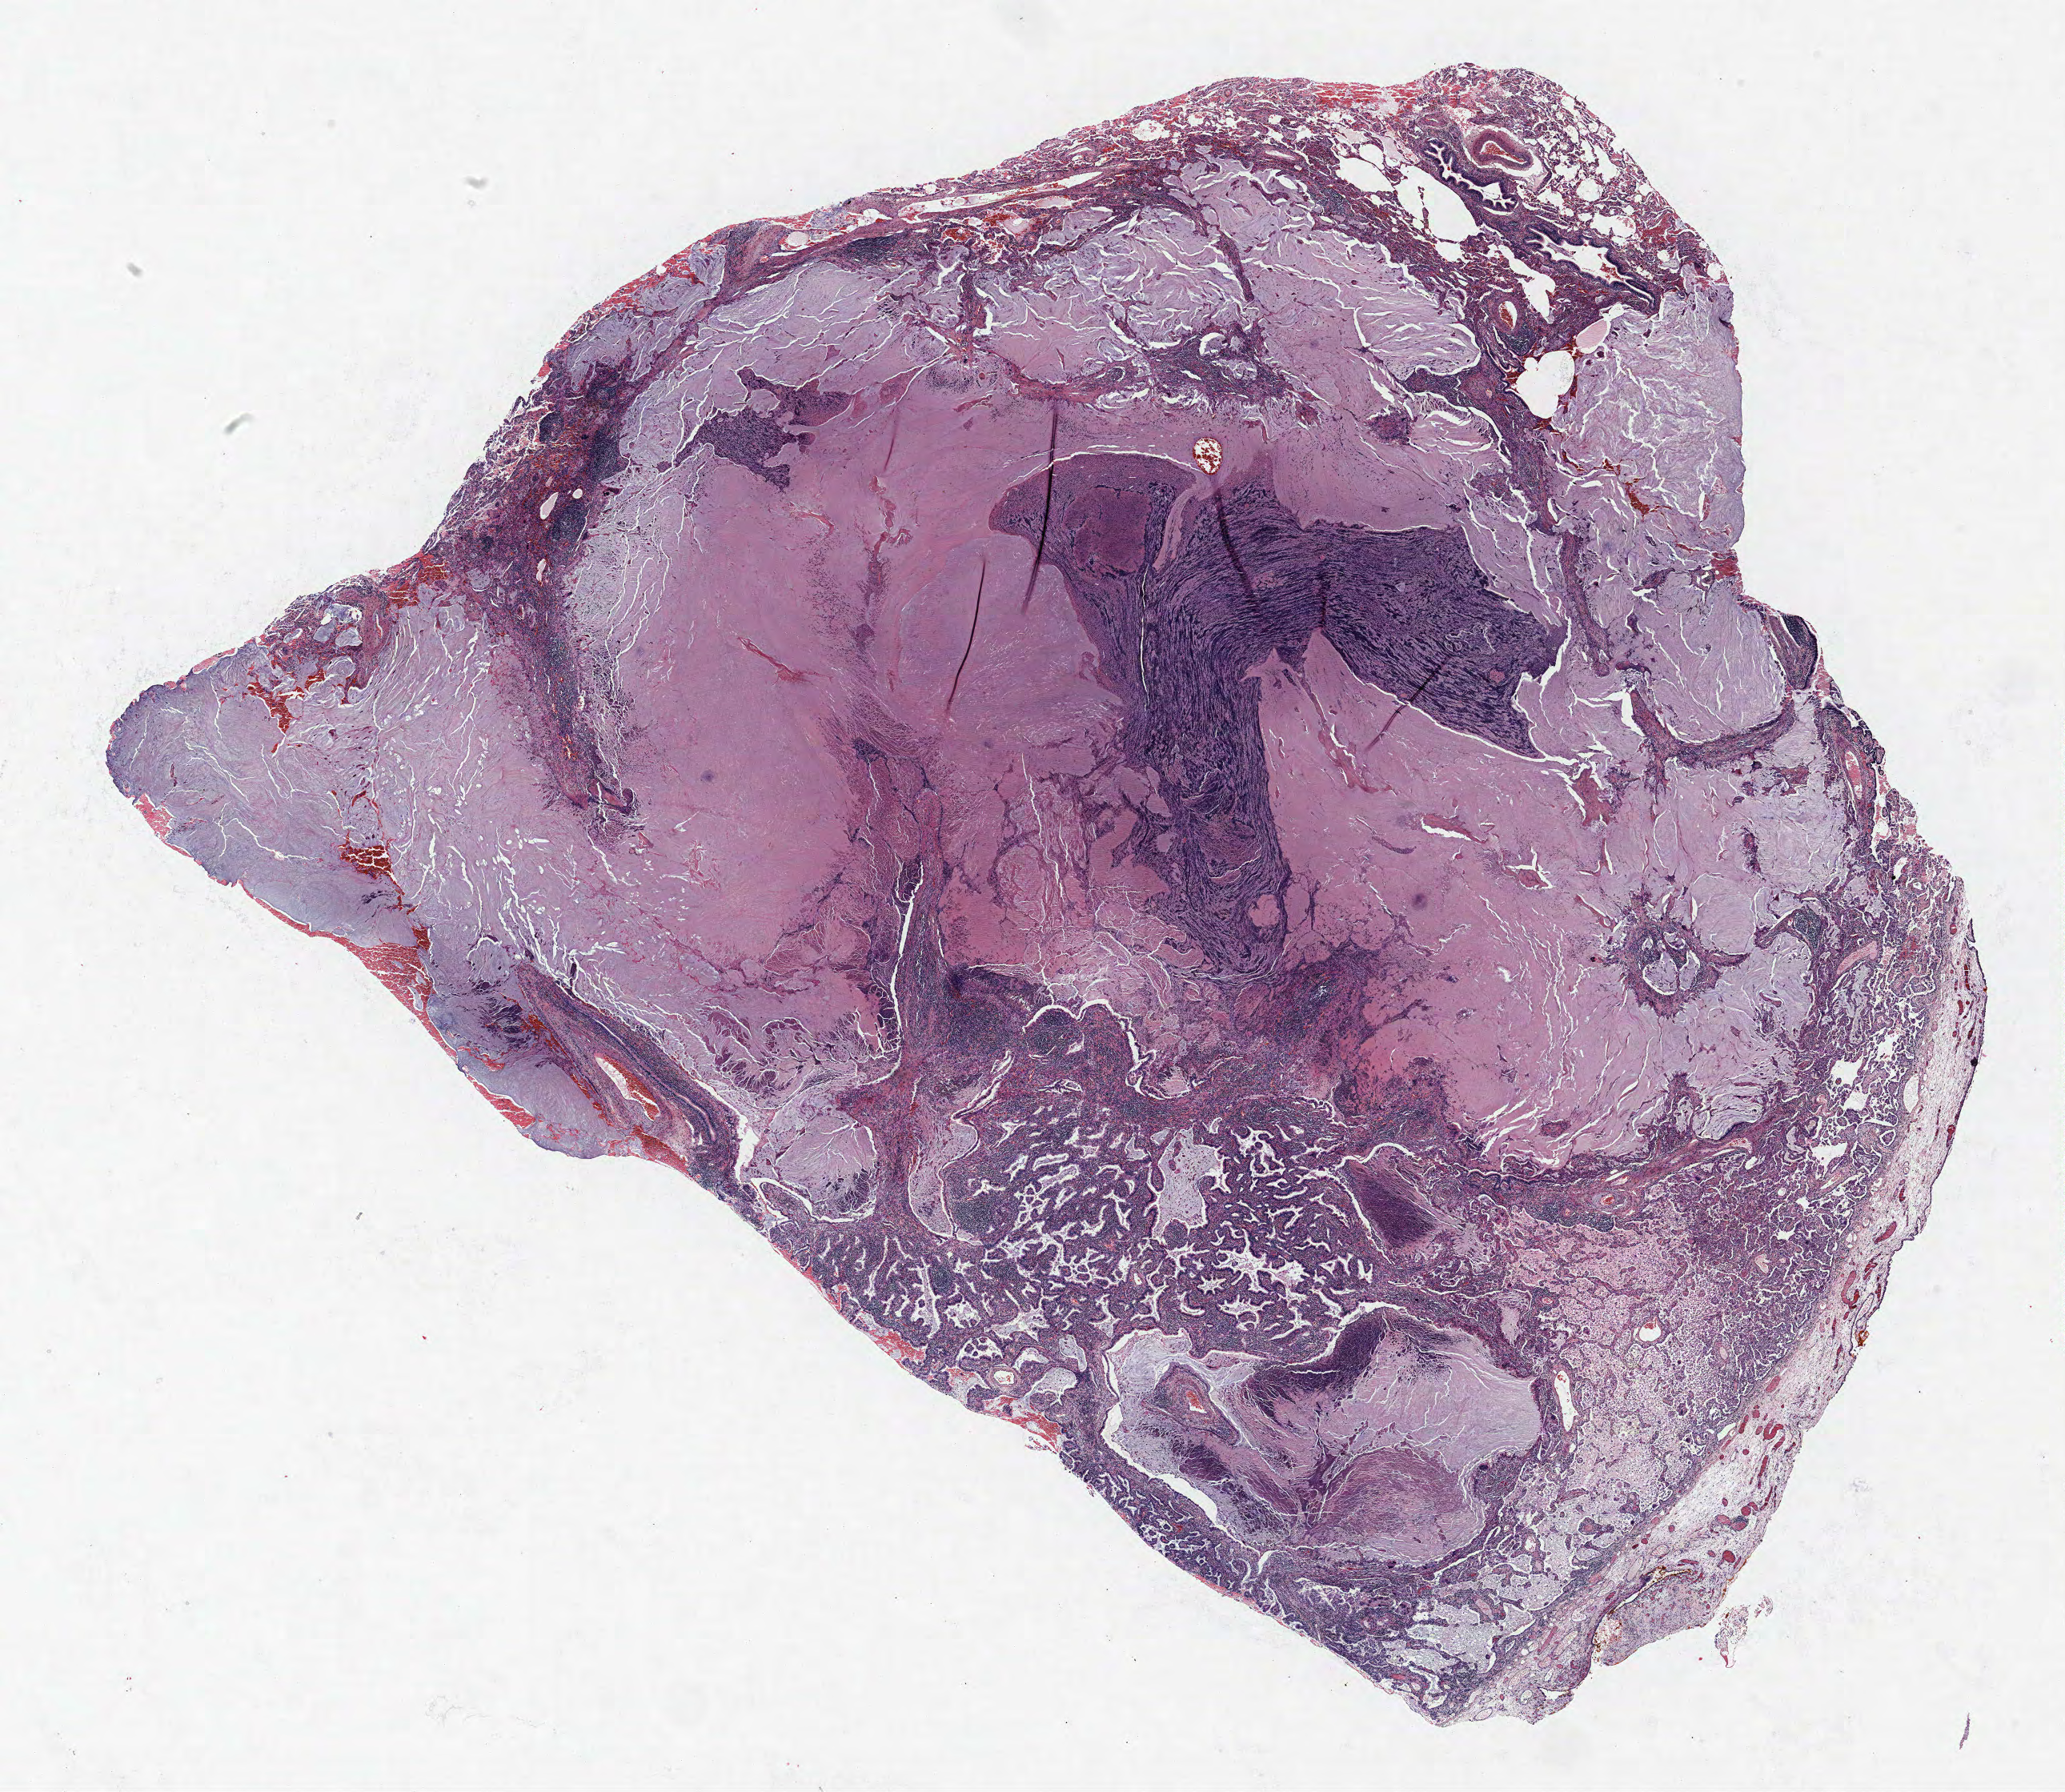
Whole-slide histology image, H&E-stained — low-resolution overview of the scanned area, about 20.6 x 17.9 mm (slide scanned at 40x). FFPE section. Lung tissue. Female patient, aged 68 at enrolment. Current smoker at enrolment. Grade: well differentiated (G1).
* tumour size (pathology): 25 mm
* stage (AJCC 6th edition): IA
* primary tumour location (clinical record): right lower lobe
* participant's lung-cancer diagnosis: Adenocarcinoma, NOS (ICD-O-3 8140/3)